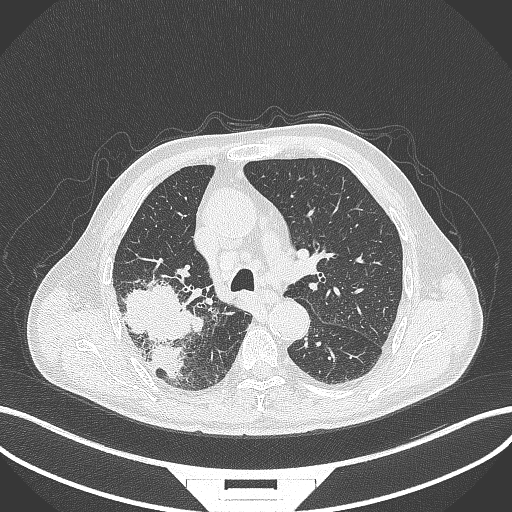
Chest CT, one axial slice; slice 276 of 429 in the series (ordered by position); reconstruction kernel B70f; lung window (W 1500 / L -600 HU); 1 mm slice thickness; 512 × 512 image matrix. Male patient, age 72 years. Case-level facts recorded for this patient, not image findings: clinical TNM (as recorded): T3 N2 M0.
Structures marked on this image (bounding box drawn by a radiologist):
- lung tumour (recorded histology: adenocarcinoma): bounding box [x1, y1, x2, y2] px = [121, 280, 209, 383]